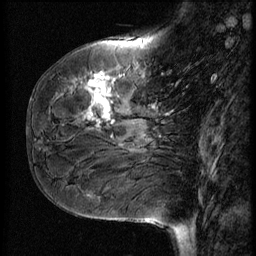
Breast MRI (dynamic contrast-enhanced), one sagittal slice; slice 21 of 56 in the series (ordered by position); 3 images stored at this slice position (order not interpretable as contrast timing); 1.5 T; TE 4.2 ms, TR 9 ms; 2.5 mm slice thickness; 256 × 256 image matrix. Patient: female, 51 years. From the clinical record (not read from this slice): setting: breast cancer imaged before/during neoadjuvant chemotherapy; receptor status: HR-positive, HER2-negative.
Outlined on this slice (semi-automatic segmentation, software-assisted and operator-edited):
- analysis volume of interest (the breast-tissue region the enhancement analysis was run in; not a lesion): bounding box [x1, y1, x2, y2] px = [41, 58, 167, 161]
- tumour enhancement mask (voxels above the 140 % enhancement threshold inside the analysis volume of interest): [73, 73, 116, 128]